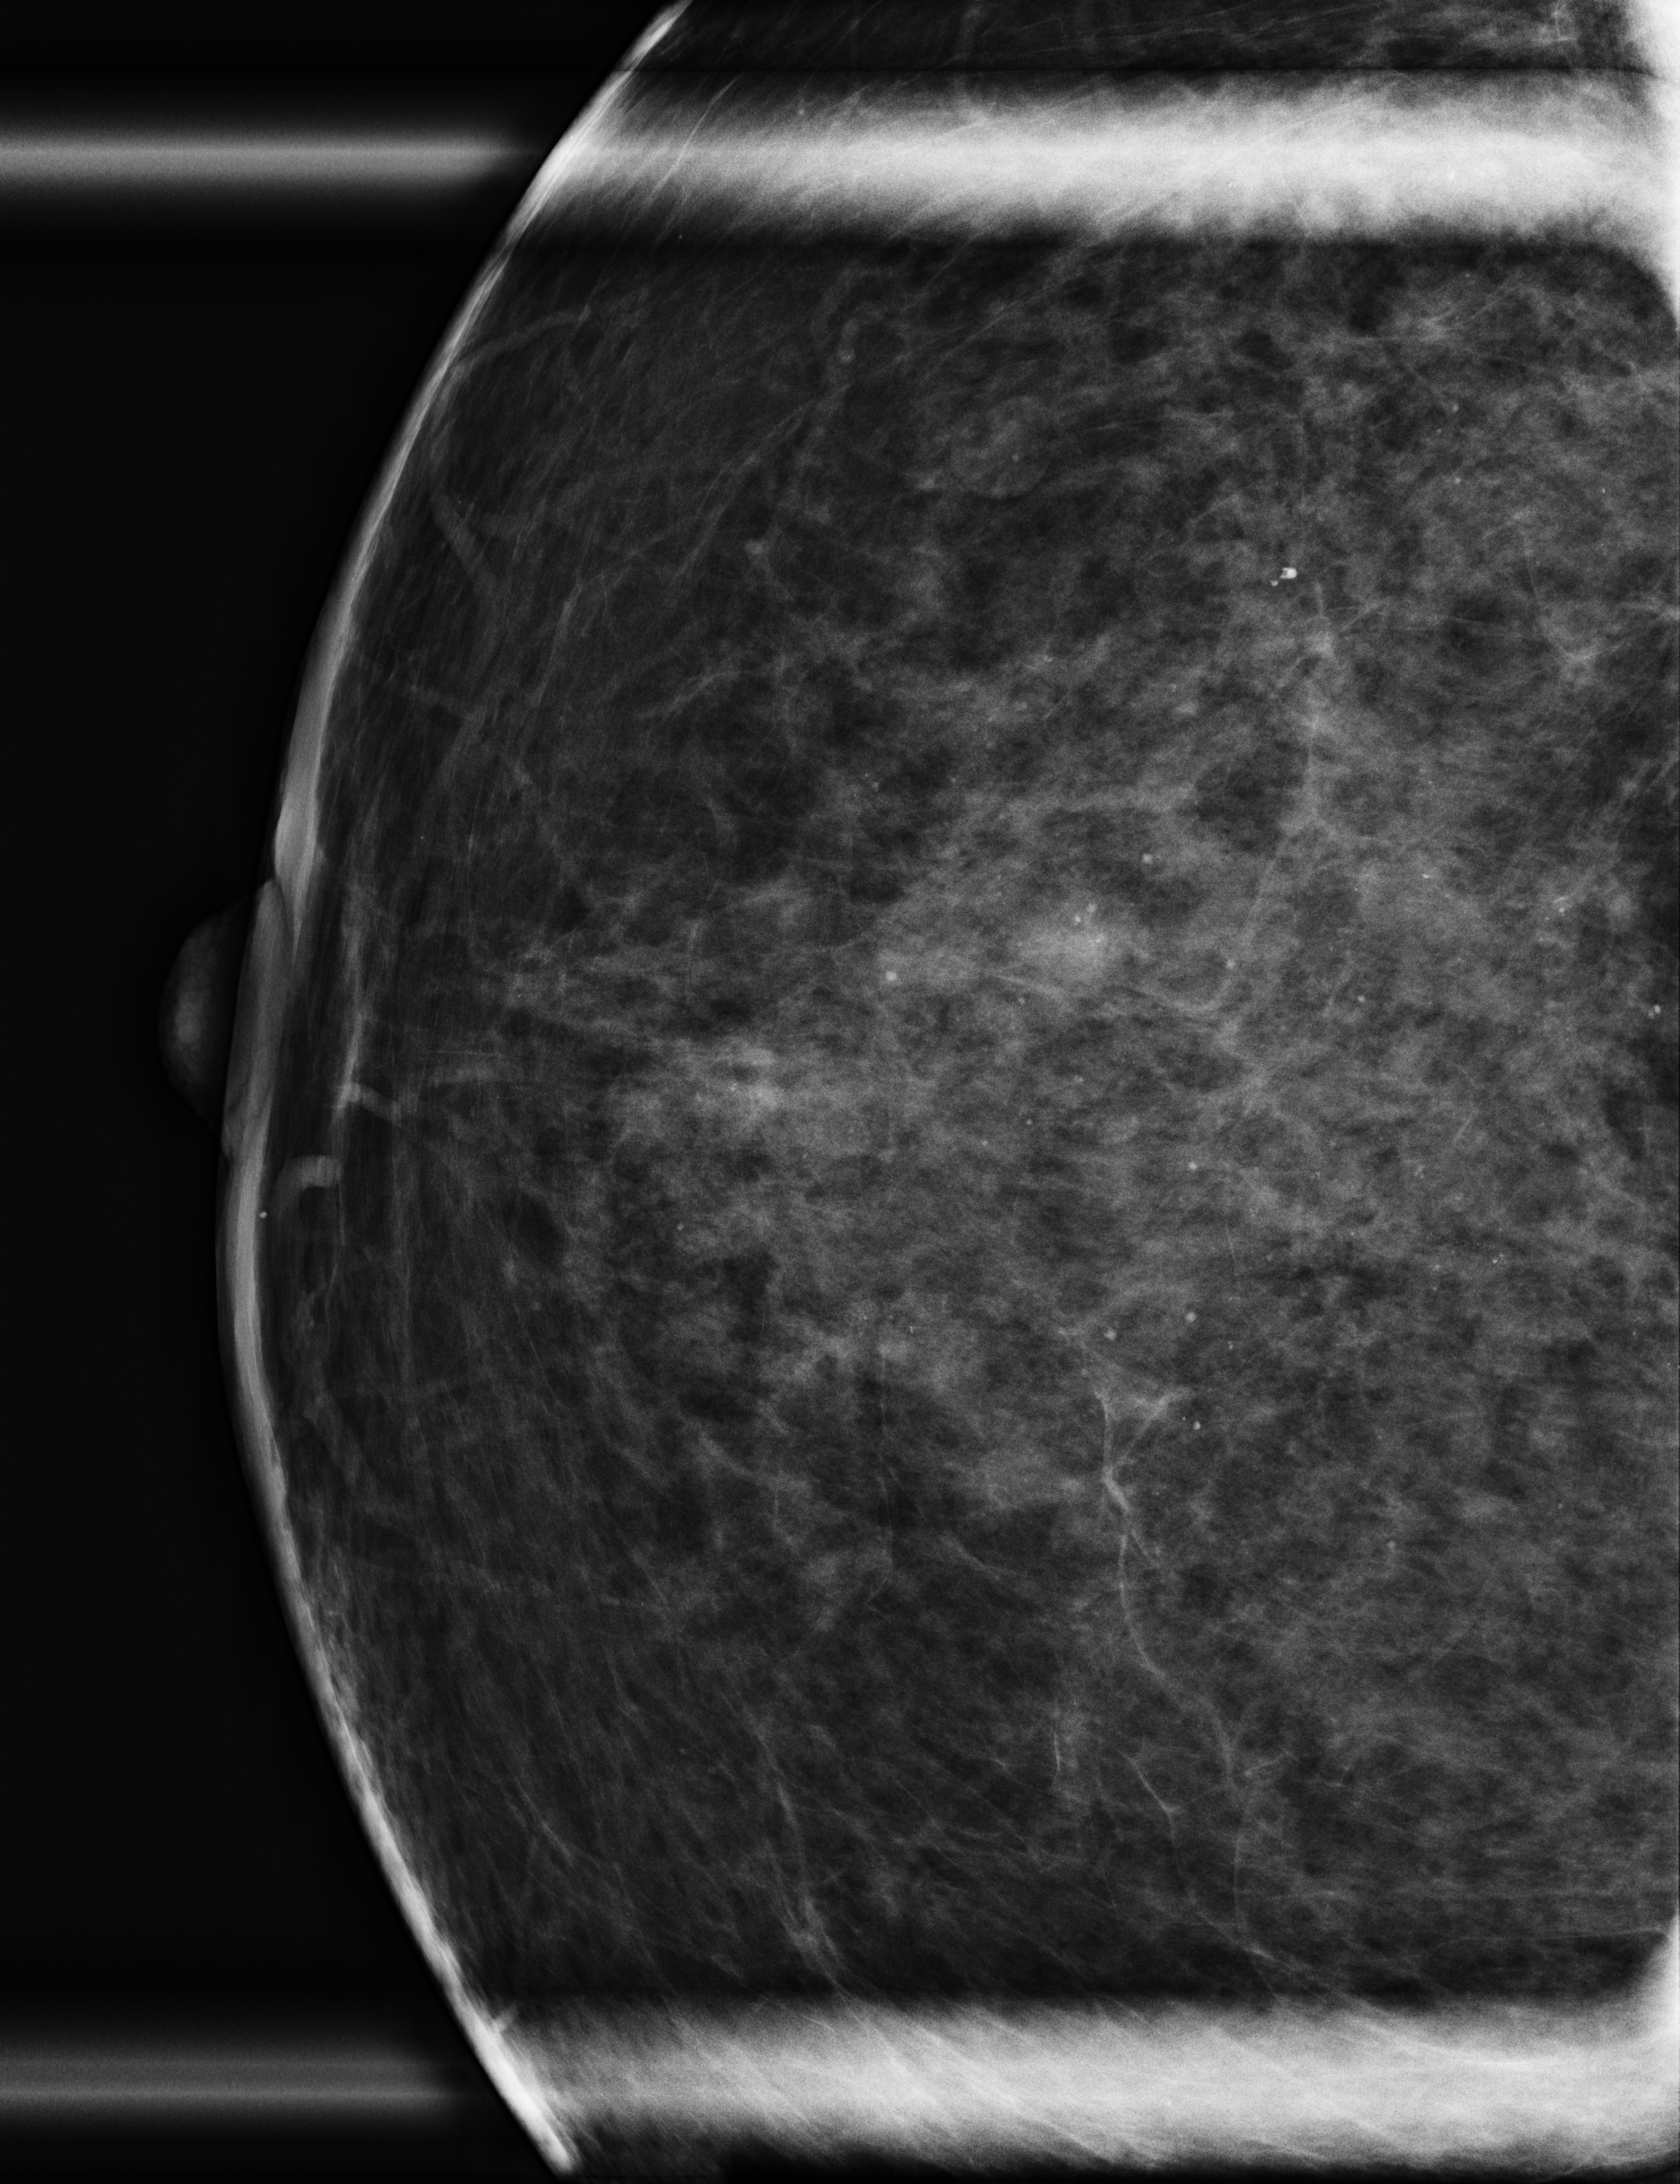
Additional work-up view, system: Selenia Dimensions. Female patient, age 71 years.
Image type: full-field digital mammogram. Breast: right. Projection: craniocaudal (CC) view, magnification. BI-RADS breast density category at the screening exam (both breasts, scale 1–4): 3. Final BI-RADS category for the screening round (tomosynthesis exam, both breasts): category 1. Recall: recalled for additional imaging after this screen.